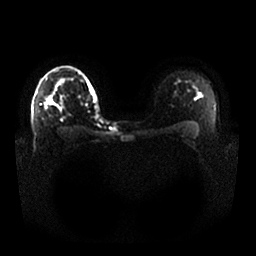
Breast MRI, one axial slice; position 19 of 25 along the scan axis; diffusion-weighted series; image 2 of 4 stored at this slice position (different b-values; order by instance number); 1.5 T; 4 mm slice thickness; 256 × 256 image matrix, field of view 370 × 370 mm. Female patient.
Annotated regions visible in this slice (expert manual segmentation):
- tumour on diffusion-weighted imaging: bounding box <48,100,50,104> (left, top, right, bottom; pixels)